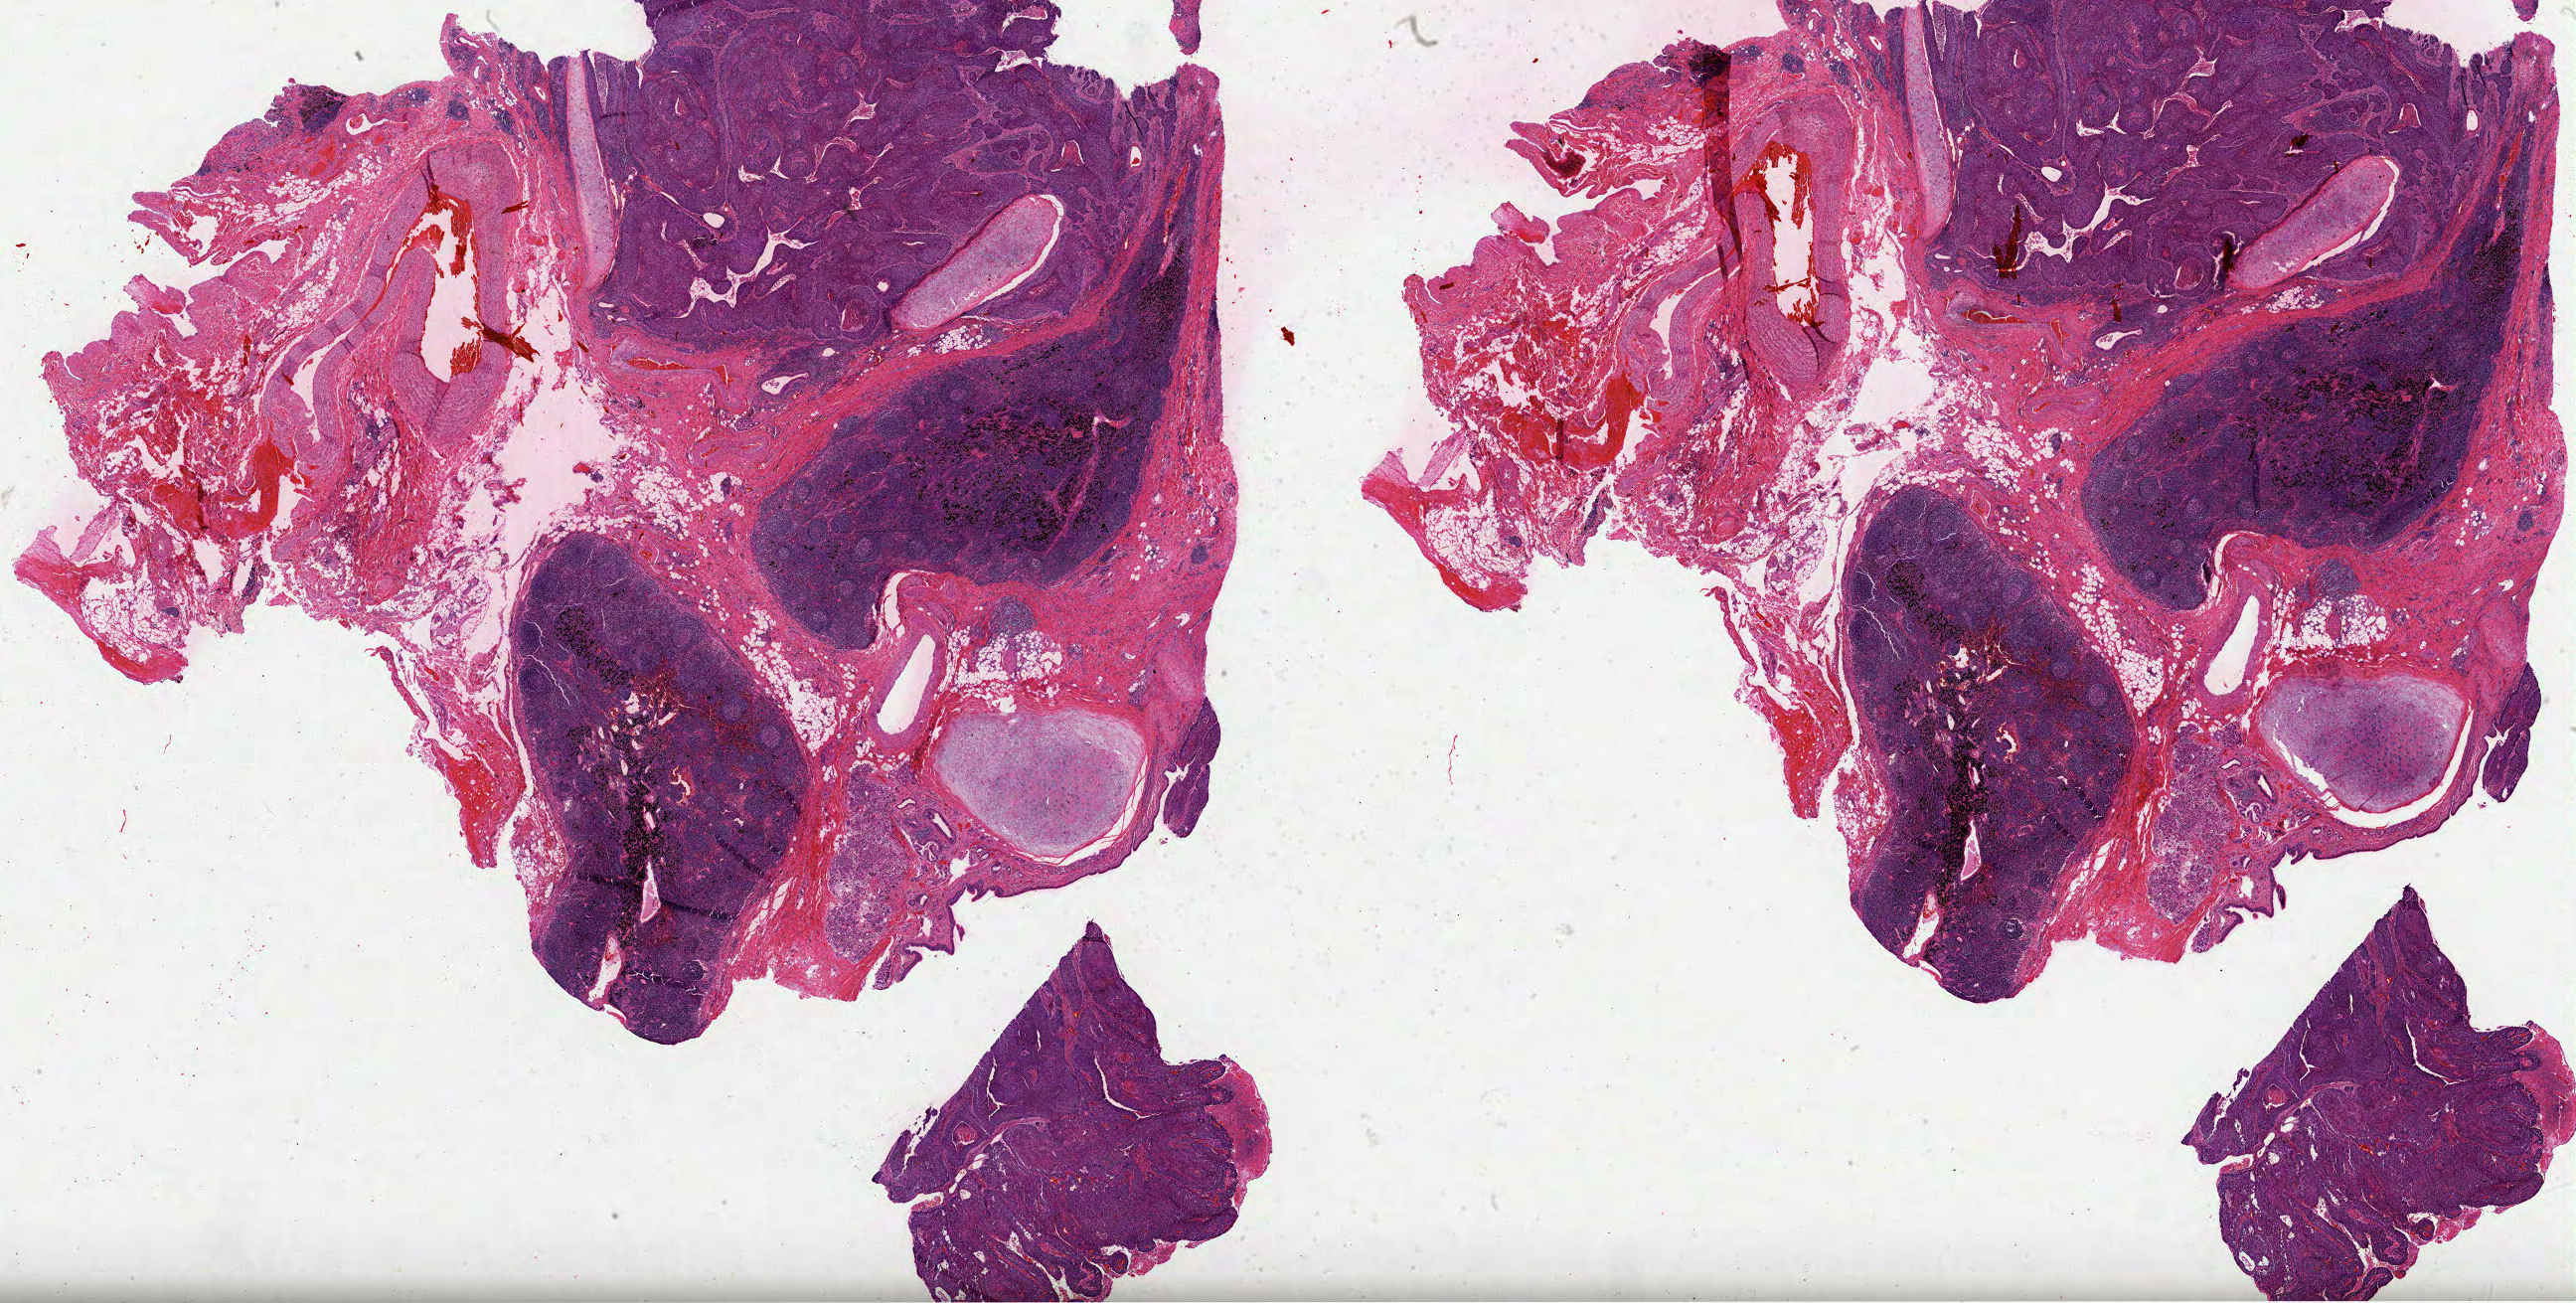
H&E-stained whole-slide image — a low-resolution overview of the entire scanned area, about 41.8 x 21.2 mm. FFPE section. Primary tumour sample from the lung. Patient: male, age at initial diagnosis 66 years.
TNM: T2 N2 M0. AJCC pathologic stage: IIIA (6th edition). Pathologic diagnosis: Squamous cell carcinoma, NOS (upper lobe, lung).